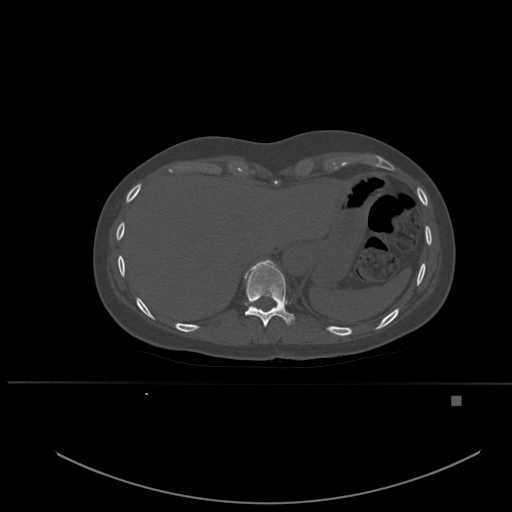
CT including the spine, one axial slice; slice 289 of 651 in the series (ordered by position); bone window (W 1800 / L 400 HU); 1.5 mm slice thickness; 512 × 512 image matrix, field of view 443 × 443 mm. Female patient, age 49 years. From the clinical record (not read from this slice): primary cancer: breast.
Structures marked on this image (semi-automatic segmentation, software-assisted and operator-edited):
- T10 vertebra: box from (x=244, y=260) to (x=295, y=327) px